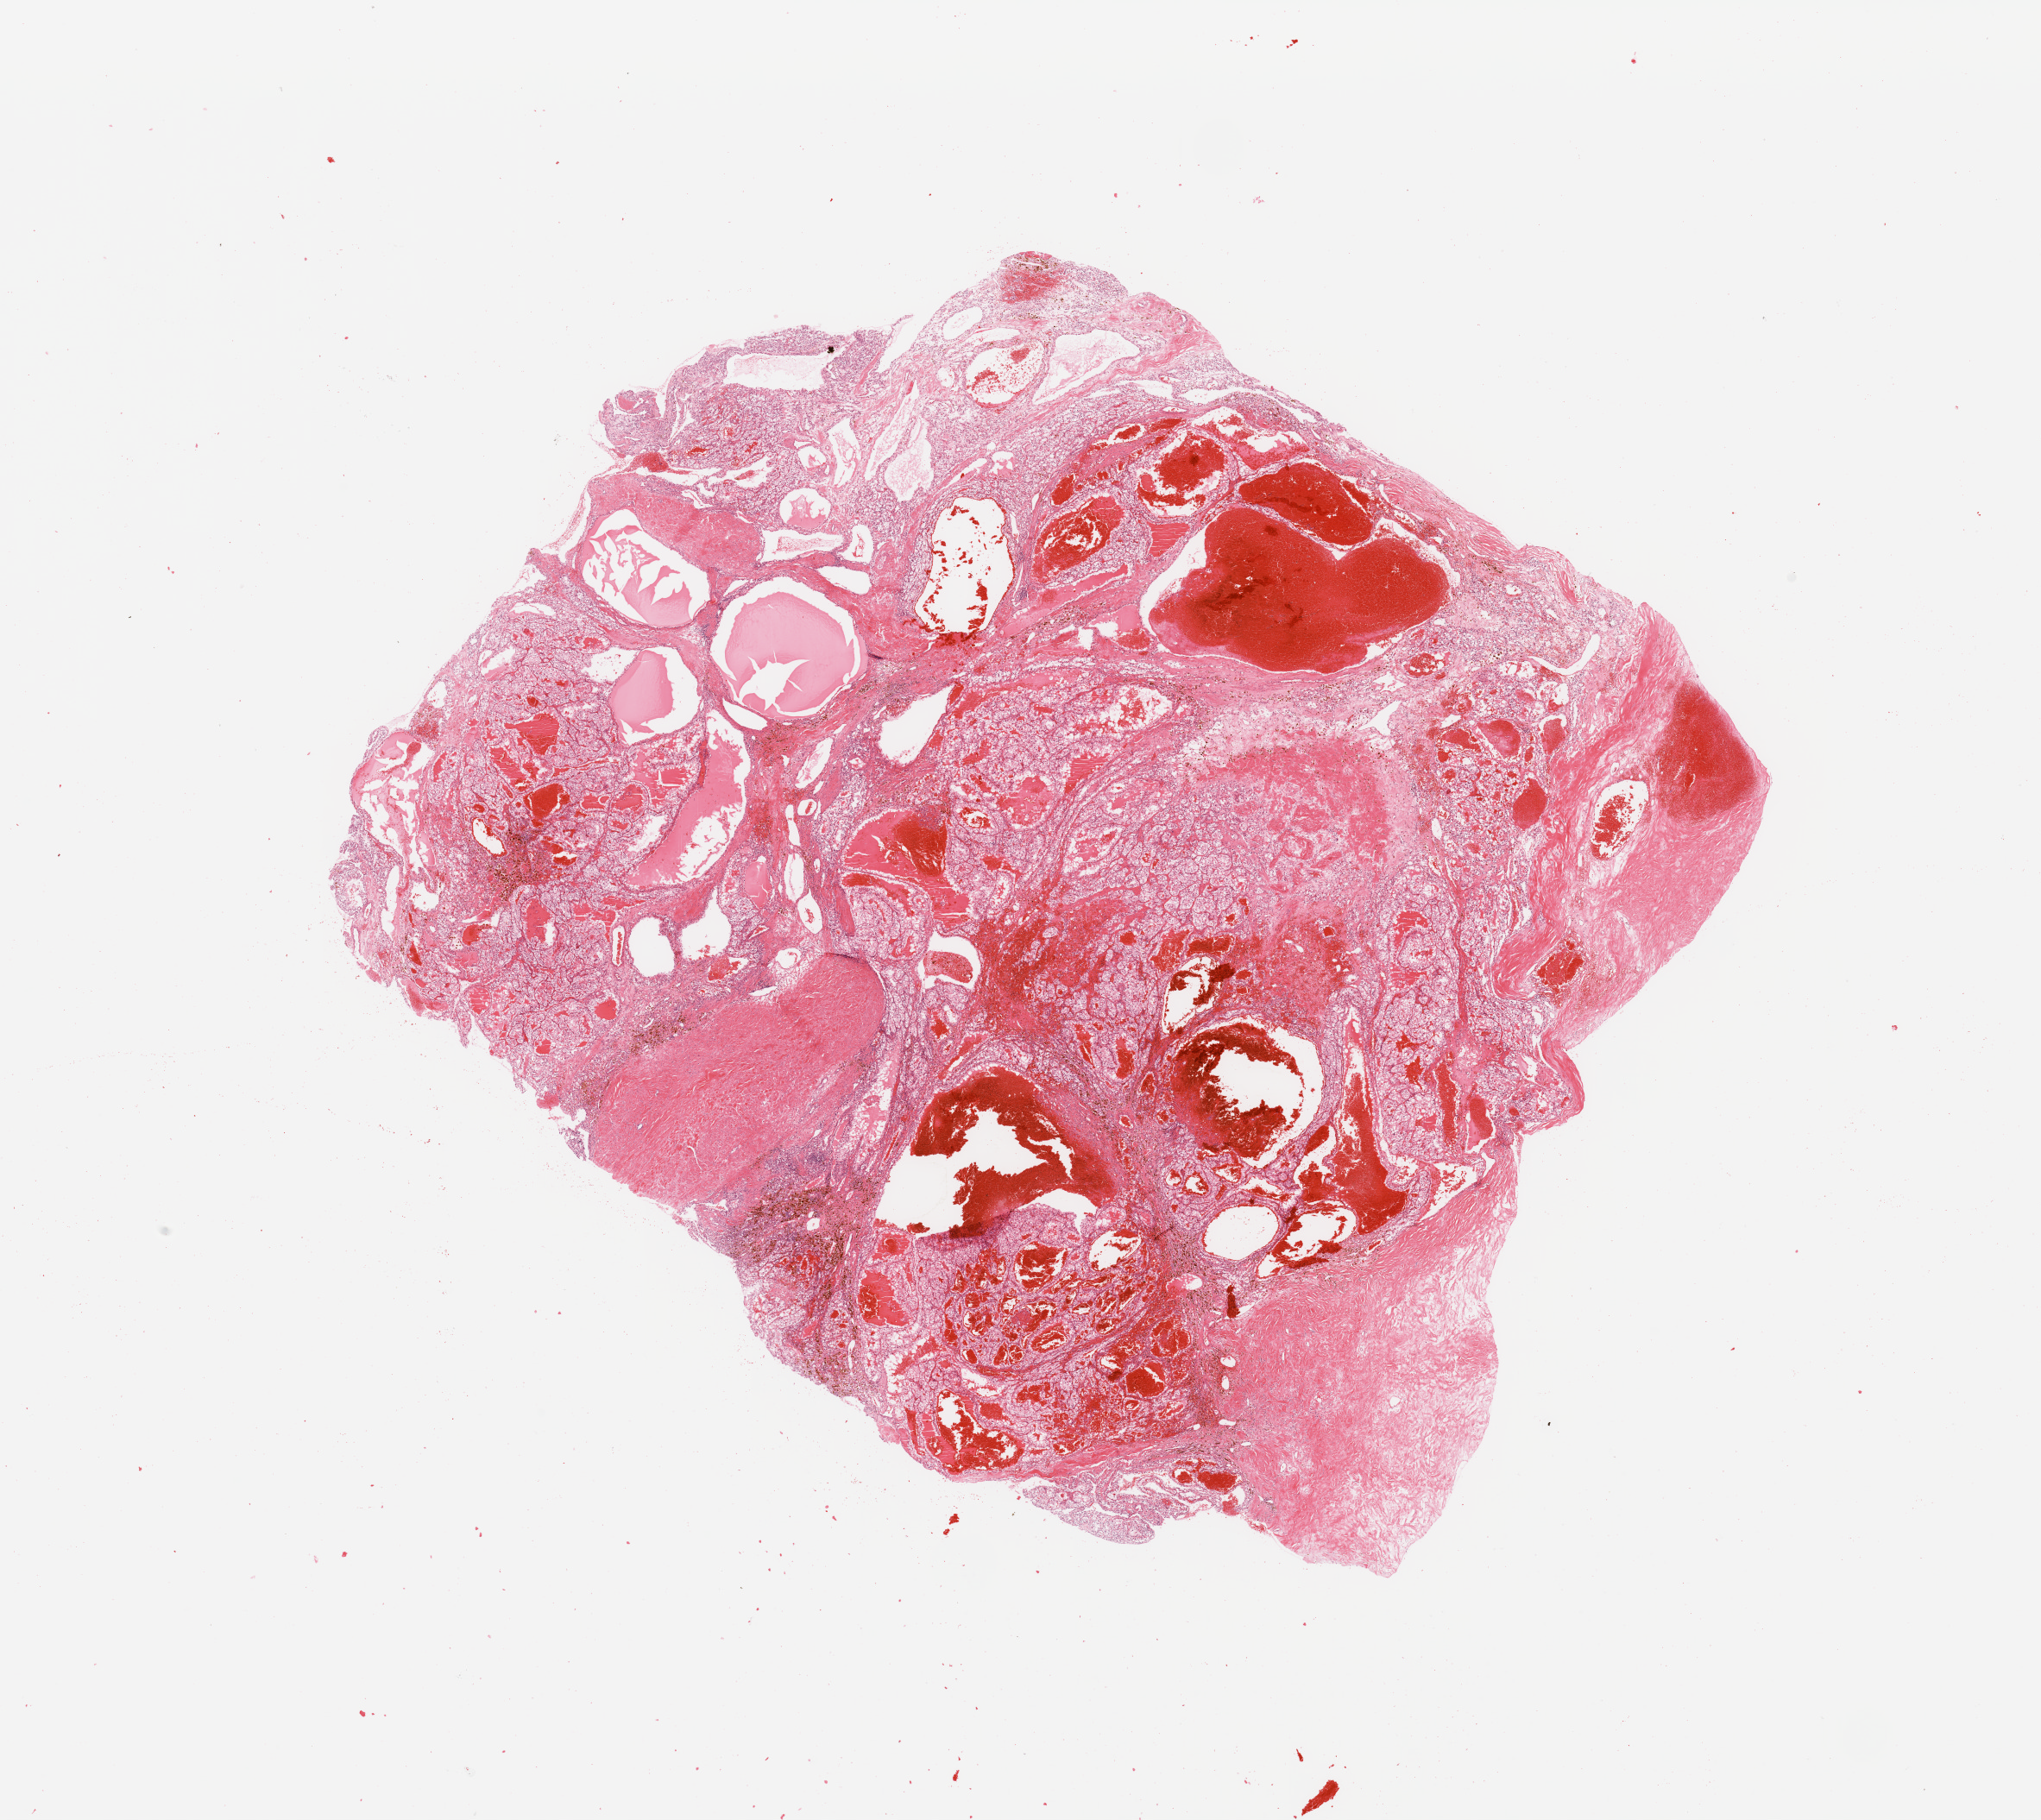
Digitized H&E tissue section (whole slide), whole scanned area (about 18.7 x 16.7 mm, slide scanned at 20x) shown as a low-resolution overview, tumour tissue sample, sampled site: kidney. Patient: female, age 55 years. Histologic grade: G3 (poorly differentiated). Composition of this section per pathologist review: tumour nuclei 80%, necrosis 15%.
Diagnosis: Renal cell carcinoma, NOS. AJCC pathologic stage: IV.